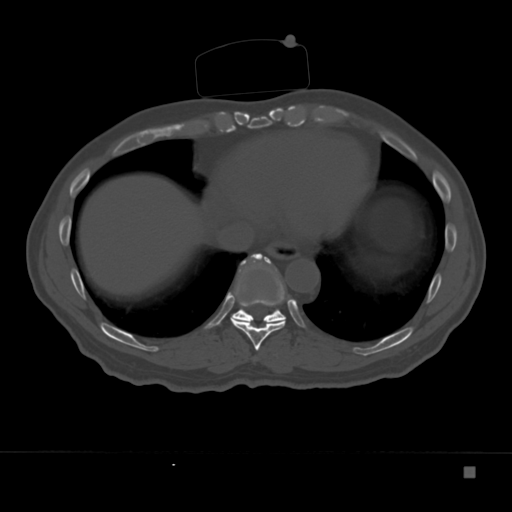
CT including the spine, one axial slice; position 183 of 332 along the scan axis; reconstruction kernel Br40s; 120 kVp; bone window (W 1800 / L 400 HU); 1.5 mm slice thickness; 512 × 512 image matrix. Male patient, age 72 years. Case-level facts recorded for this patient, not image findings: primary cancer: skeletal.
Outlined on this slice (semi-automatic segmentation, software-assisted and operator-edited):
- T10 vertebra: bounding box [x1, y1, x2, y2] px = [230, 254, 285, 322]
- T9 vertebra: [231, 253, 289, 351]